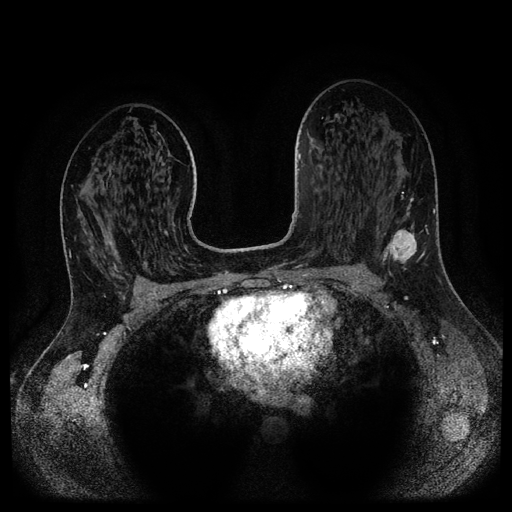
Breast MRI (dynamic contrast-enhanced, multi-phase), one axial slice. Slice 64 of 116 in the series (ordered by position). Dynamic contrast-enhanced series, time point 2 of 5 at this slice position (early post-contrast). 1.5 T. TE 2.6 ms, TR 5.3 ms. 2.1 mm slice thickness. 512 × 512 image matrix. Patient: female, 37 years.
Annotated regions visible in this slice (semi-automatically segmented with operator editing):
- breast lesion (labelled 'tumour' in the annotation; benign lesions carry a separate 'benign' label): box from (x=380, y=193) to (x=421, y=274) px